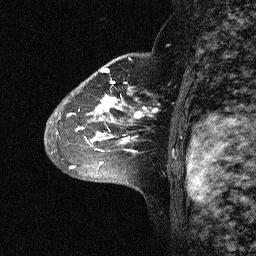
Breast MRI (dynamic contrast-enhanced), one sagittal slice; position 44 of 64 along the scan axis; dynamic contrast-enhanced study with each time point stored as its own series, time point 2 of 3 at this slice position (early post-contrast, ordered by acquisition time); 1.5 T; TE 4.5 ms, TR 11 ms; 2.06 mm slice thickness; 256 × 256 image matrix, field of view 200 × 200 mm. Patient: female, 46 years. Case-level facts recorded for this patient, not image findings: setting: breast cancer imaged before/during neoadjuvant chemotherapy; receptor status: HER2-positive.
Structures marked on this image (semi-automatically segmented with operator editing):
- analysis volume of interest (the breast-tissue region the enhancement analysis was run in; not a lesion): box from (x=43, y=72) to (x=164, y=177) px
- tumour enhancement mask (voxels above the 90 % enhancement threshold inside the analysis volume of interest): (x=68, y=72)–(x=160, y=168)